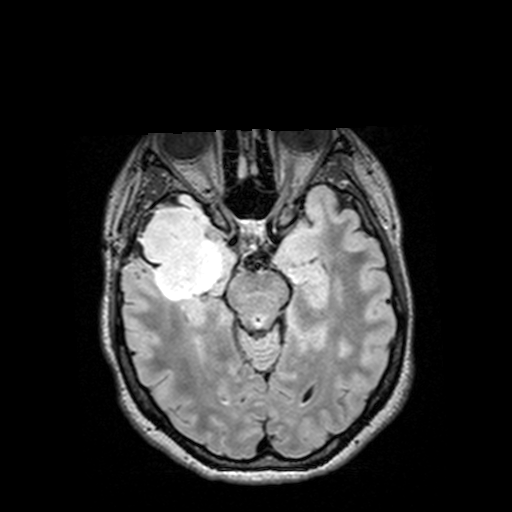
Brain MRI from a brain-tumour surgery series, one axial slice. Slice 88 of 144 in the series (ordered by position). T2 FLAIR. 1 mm slice thickness. 512 × 512 image matrix, field of view 250 × 250 mm. Case-level facts recorded for this patient, not image findings: histopathology: Astrocytoma; WHO grade: 3; IDH mutation: yes; tumour location: Right Insular Temporal.
Outlined on this slice (outlined manually by an expert reader):
- tumour: bounding box [x1, y1, x2, y2] px = [132, 193, 226, 308]